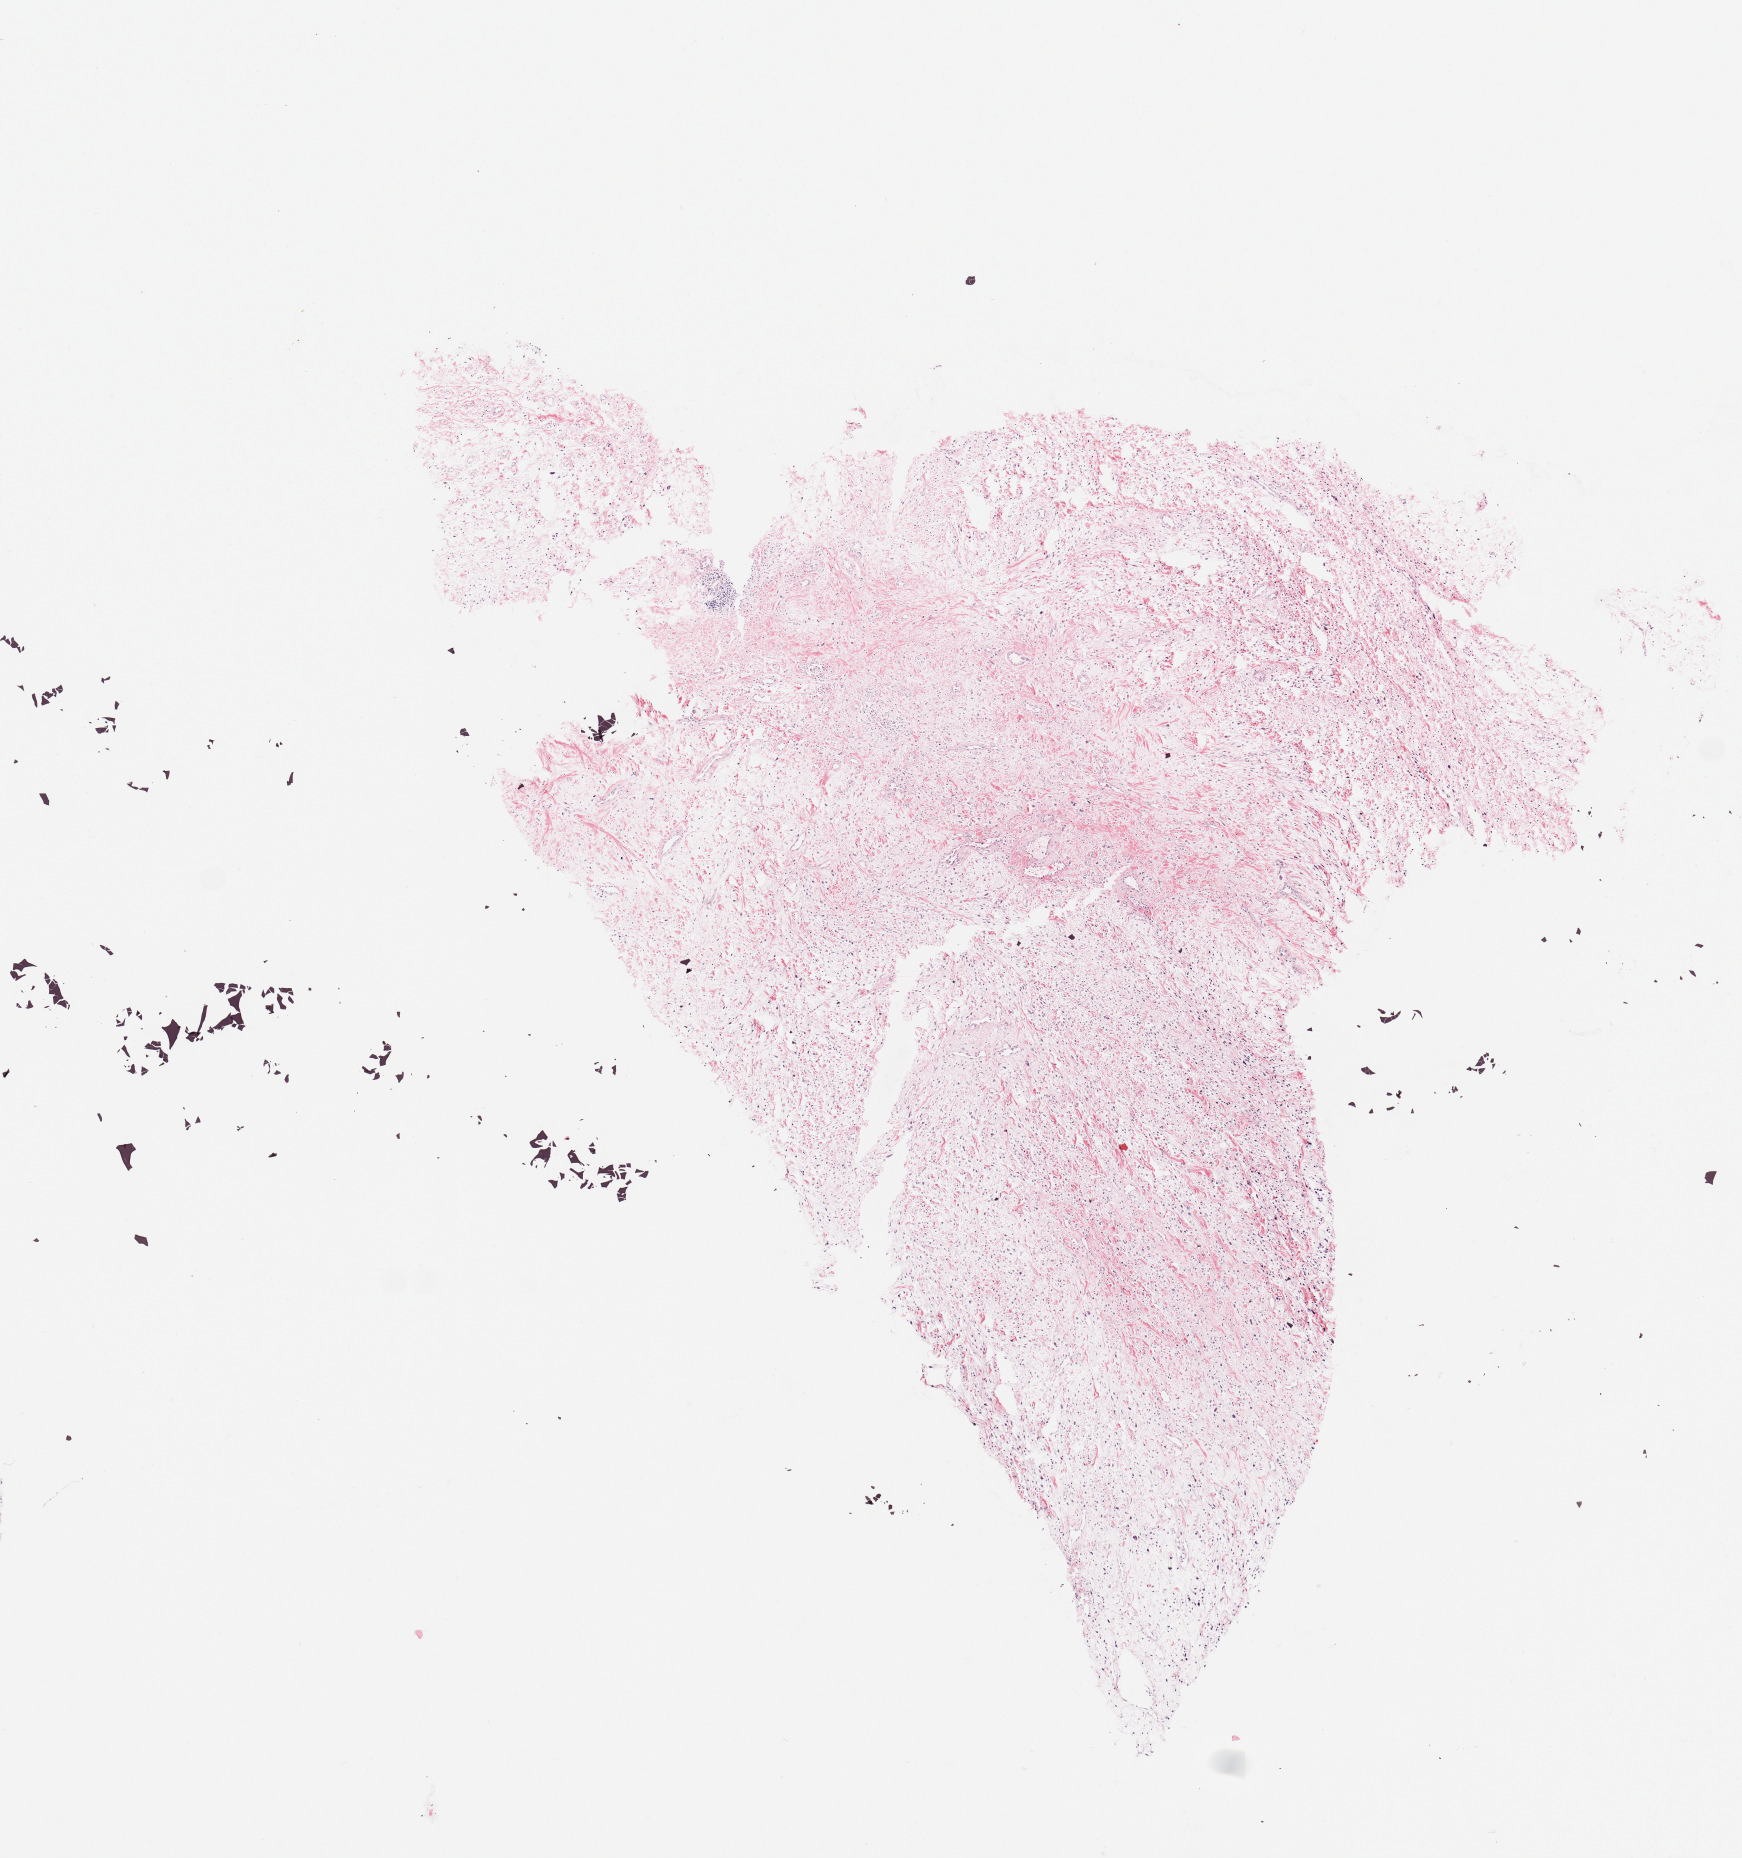
H&E whole-slide image, a low-resolution overview of the entire scanned area, about 6.9 x 7.3 mm, tumour tissue sample. Patient: male, age 67 years.
* patient diagnosis (cohort enrolment): sarcoma (site not recorded at cohort level)
* primary tumour site (as recorded): lower extremity